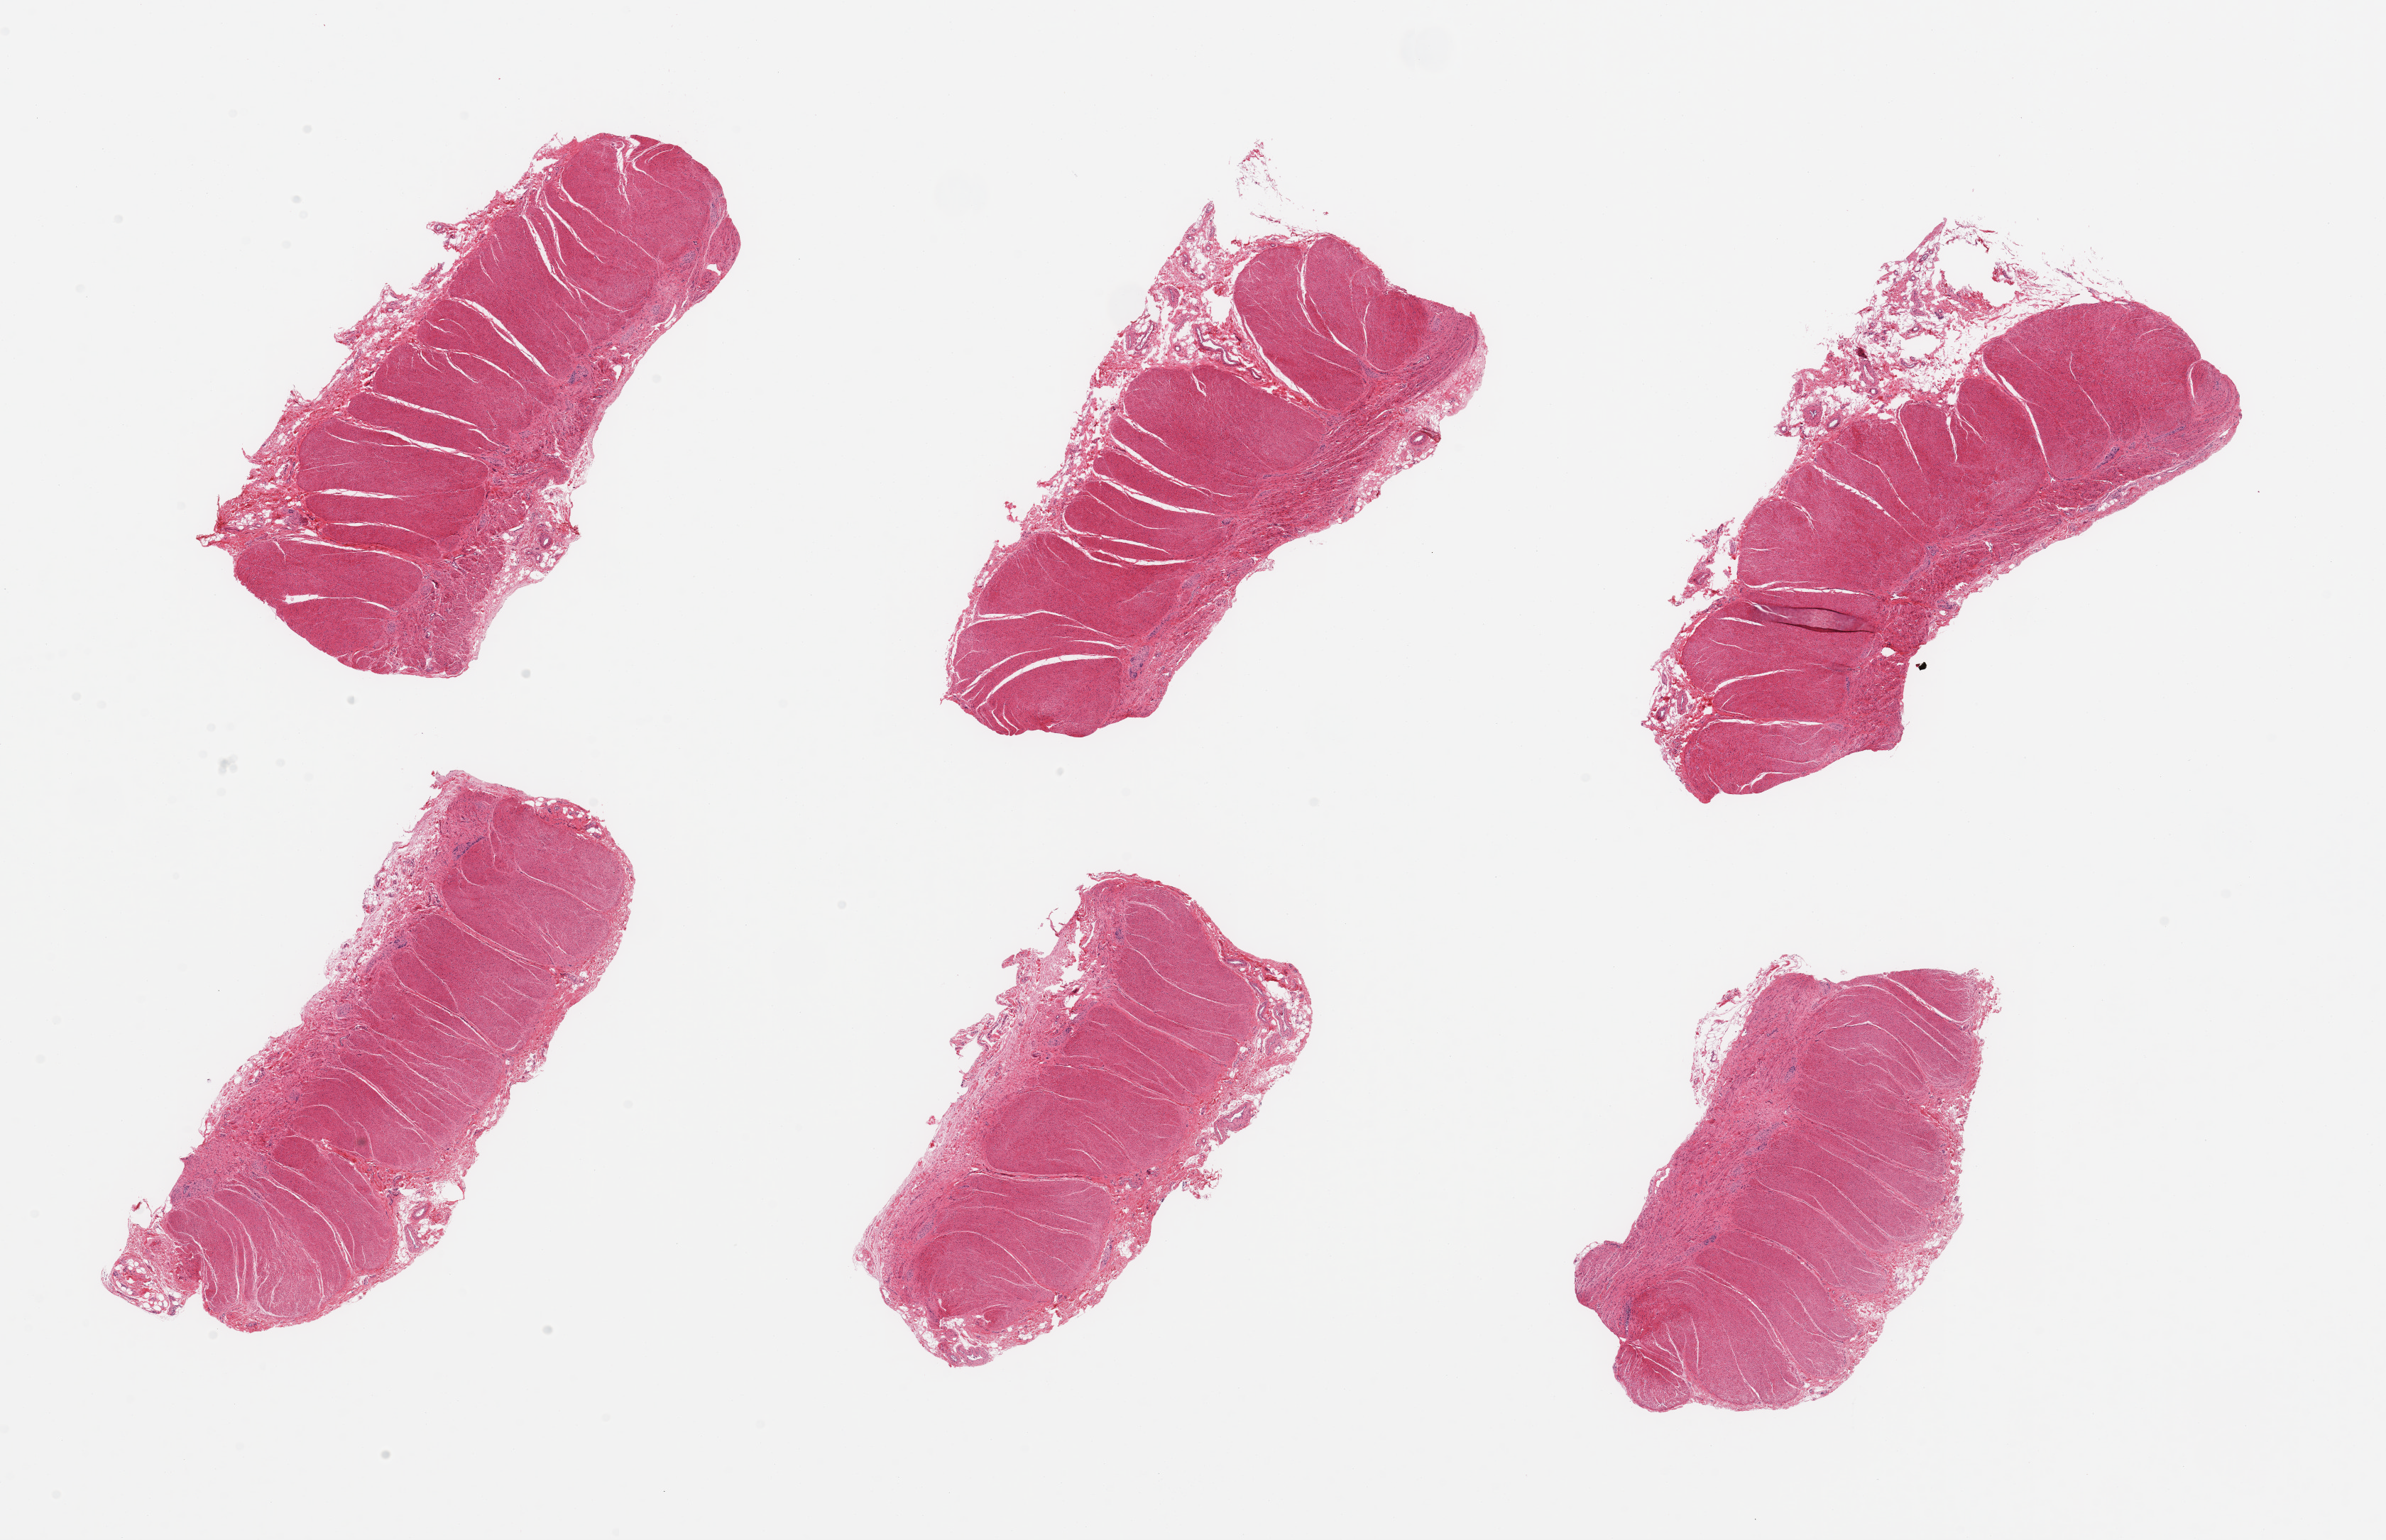
Haematoxylin and eosin whole-slide image, low-resolution overview of the scanned area, about 26.6 x 17.2 mm; PAXgene-fixed, paraffin-embedded tissue; section of sigmoid colon (target tissue); tissue donor sample. Donor: male.
Review note (as recorded): 6 pieces; target muscularis with up to 1.4 mm attached adventitia.